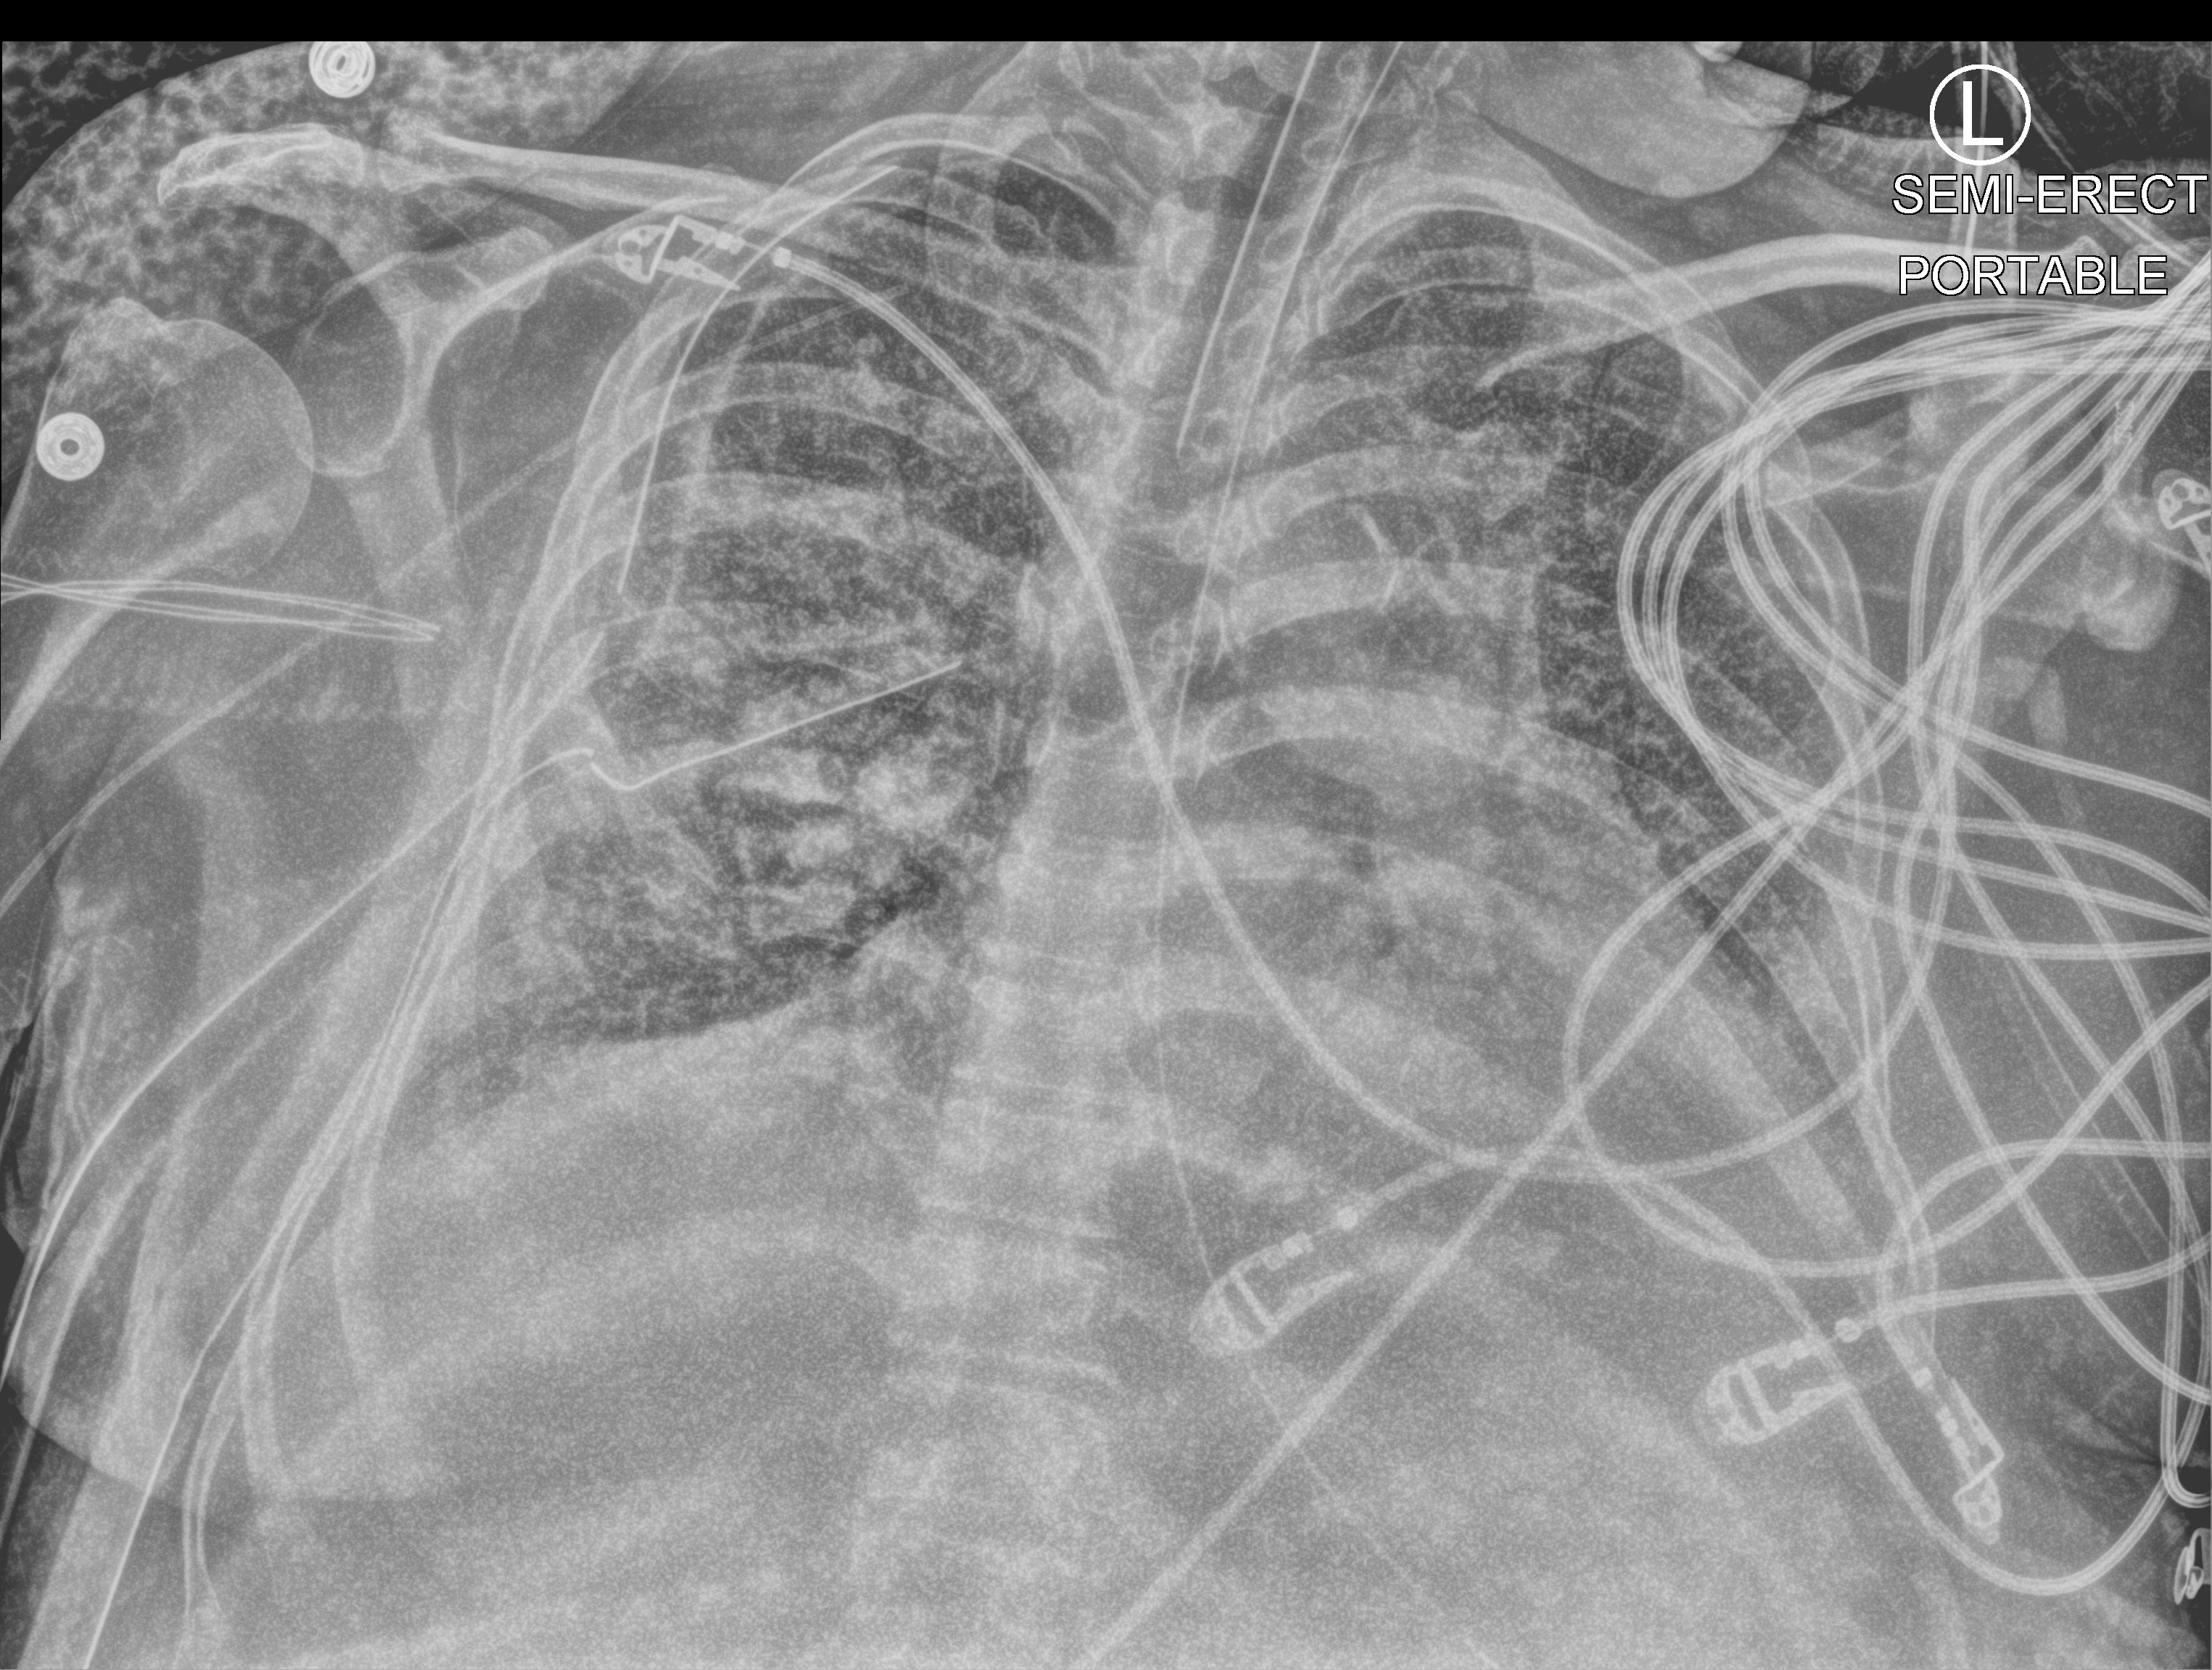
Bedside chest radiograph (computed radiography); anteroposterior (AP) projection. Patient hospitalised with COVID-19, aged 18–59 years.
Admission-level facts for this patient (not findings on this image; timing relative to this image not recorded): mechanically ventilated during this hospital stay: yes.